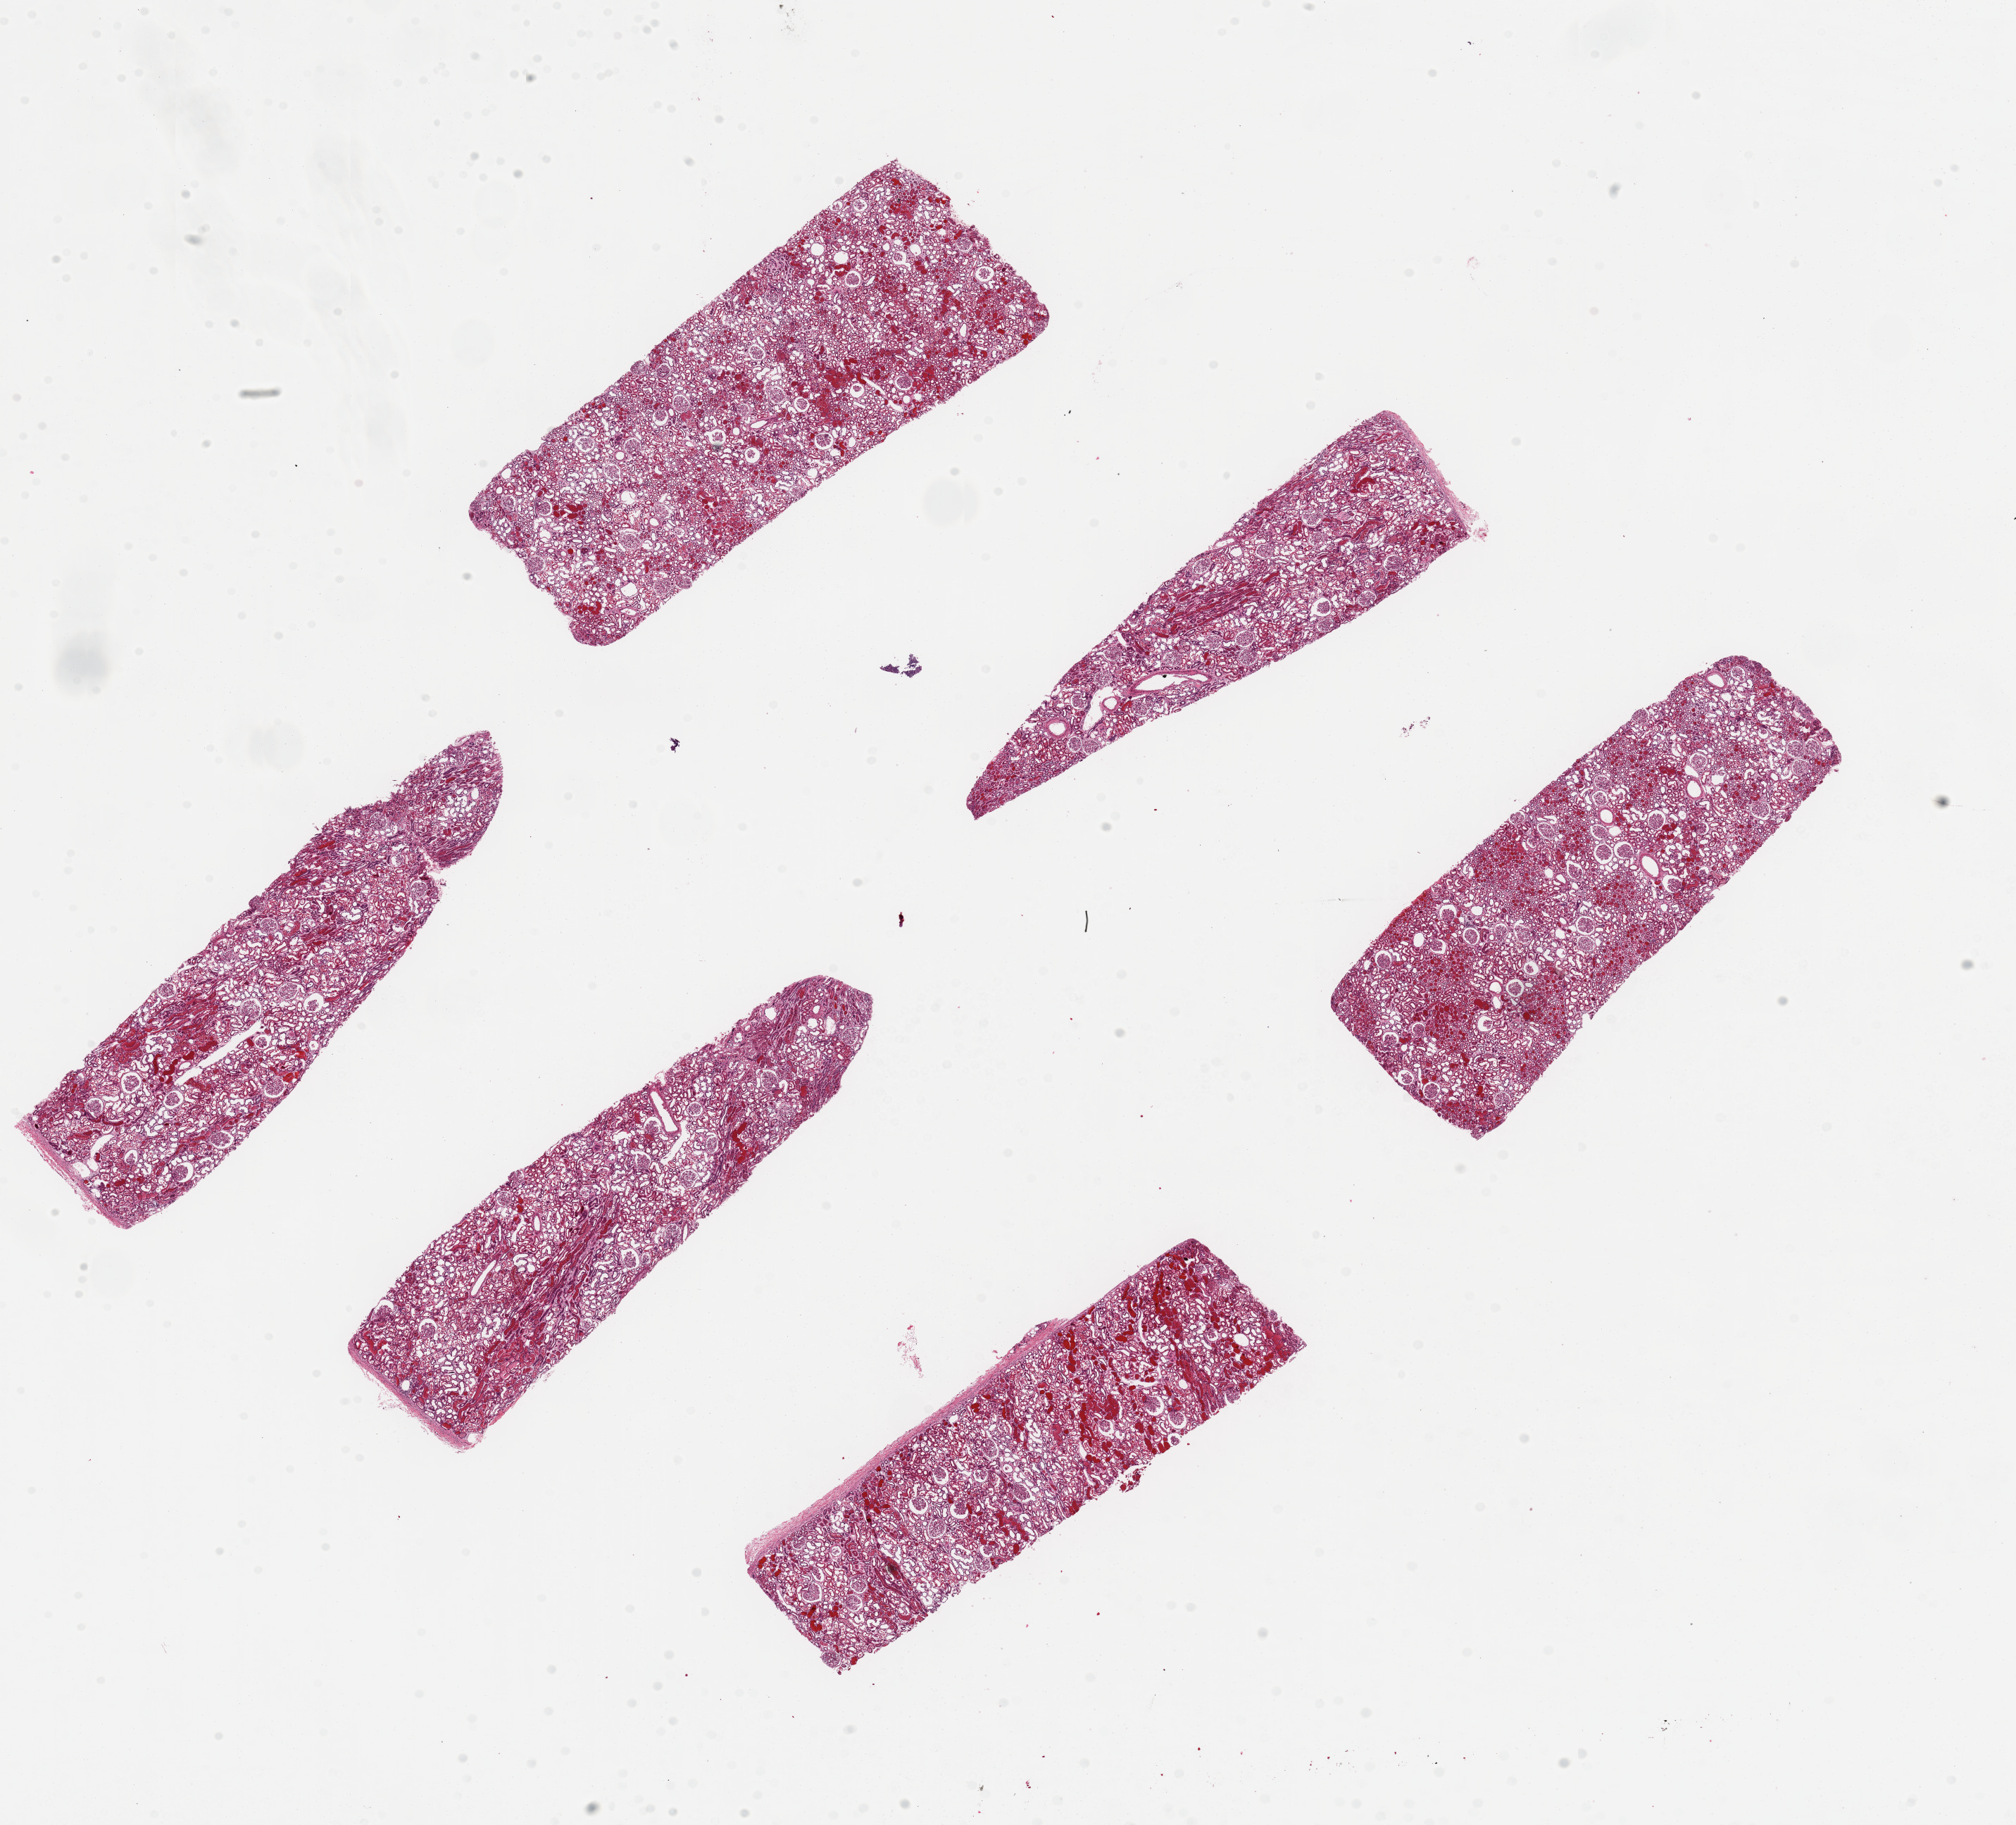
Digitized hematoxylin and eosin (H&E)-stained section, low-resolution overview of the scanned area, about 22.6 x 20.5 mm. PAXgene-fixed paraffin-embedded (PFPE) section. Sampled site (target tissue): renal cortex. Tissue donor sample.
Pathologist's review note for this sample: 6 pieces, ~6x2.5 mm; numerous red cell casts.